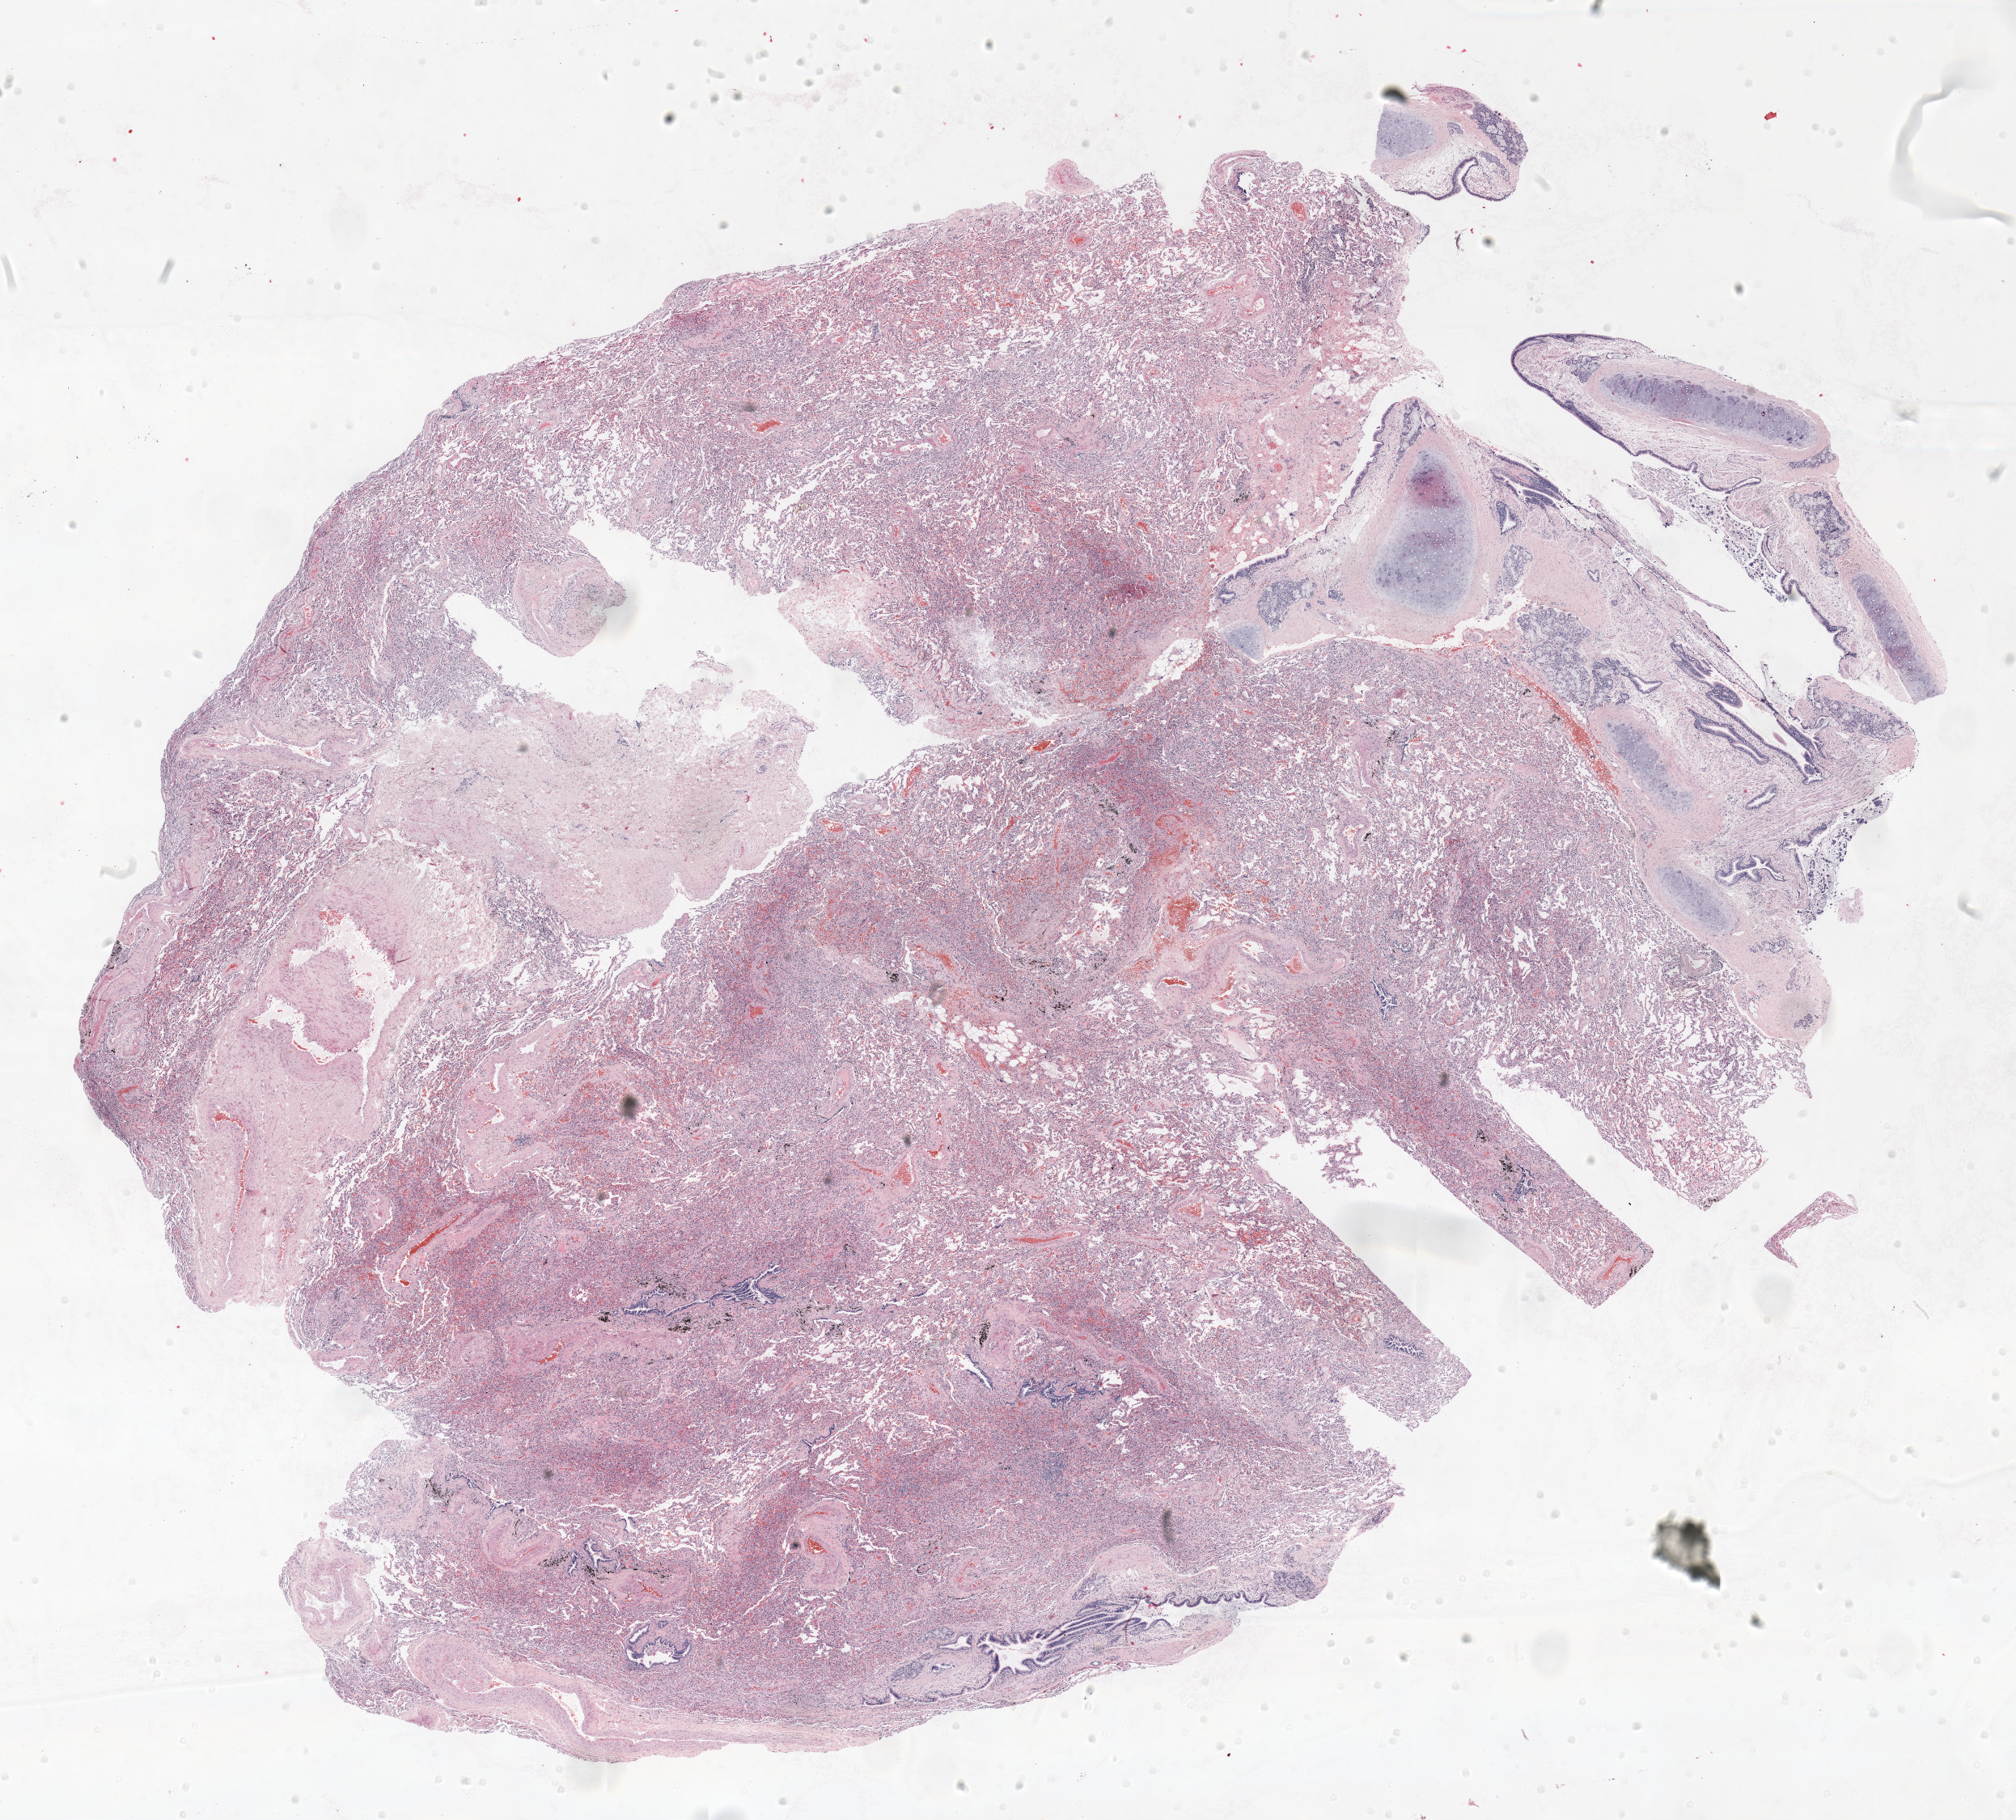
Hematoxylin and eosin (H&E) stained whole-slide image, whole scanned area (about 20.0 x 18.1 mm, acquisition: 20x scan) shown as a low-resolution overview; formalin-fixed paraffin-embedded (FFPE) section; lung. Female patient, aged 59 at enrolment. Grade: well differentiated (G1).
Participant's lung-cancer diagnosis: Bronchiolo-alveolar adenocarcinoma, NOS. Stage (AJCC 6th edition): IA. Tumour size (pathology): 10 mm. Primary tumour location (clinical record): left upper lobe.